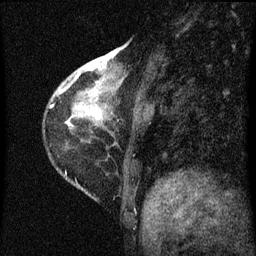
Breast MRI (dynamic contrast-enhanced), one sagittal slice; slice 18 of 60 in the series (ordered by position); dynamic contrast-enhanced series, image 2 of 3 at this slice position (ordered by acquisition); 1.5 T; TE 4.2 ms, TR 8 ms; 2 mm slice thickness; 256 × 256 image matrix, field of view 180 × 180 mm. Patient: female, 38 years.
Outlined on this slice (semi-automatically segmented with operator editing):
- analysis volume of interest (the breast-tissue region the enhancement analysis was run in; not a lesion): box from (x=67, y=44) to (x=144, y=131) px
- tumour enhancement mask (voxels above the 70 % enhancement threshold inside the analysis volume of interest): (x=76, y=68)–(x=102, y=117)